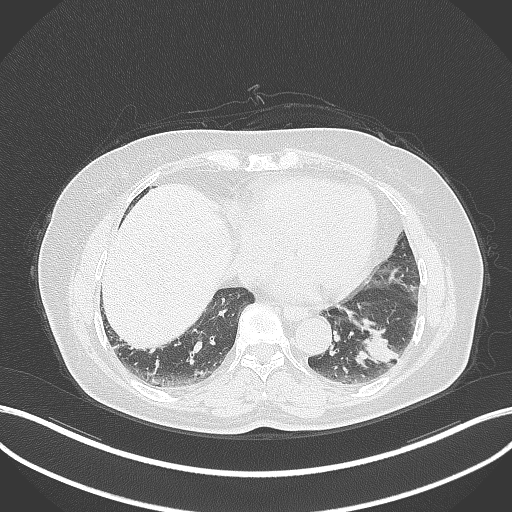
Chest CT, one axial slice. Lung window (W 1500 / L -600 HU). 1 mm slice thickness. 512 × 512 image matrix, field of view 400 × 400 mm. Female patient, age 59 years. From the clinical record (not read from this slice): clinical TNM (as recorded): T2a N0 M0; histopathological grade: G2-3.
Structures marked on this image (rectangle marked by the reading radiologist):
- lung tumour (recorded histology: adenocarcinoma): box from (x=347, y=318) to (x=400, y=369) px